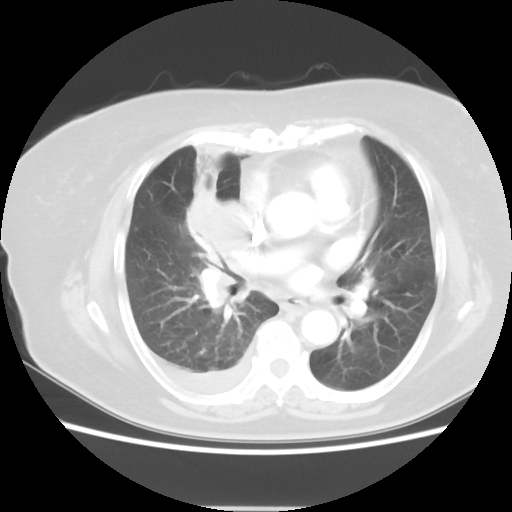
Chest CT, one axial slice. Slice 25 of 48 in the series (ordered by position). 120 kVp. Lung window (W 1500 / L -600 HU). 5 mm slice thickness. 512 × 512 image matrix, field of view 360 × 360 mm. Patient: female, 73 years. Case-level facts recorded for this patient, not image findings: clinical TNM (as recorded): T3 N3 M1b.
Outlined on this slice (bounding box drawn by a radiologist):
- lung tumour (recorded histology: small cell carcinoma): bounding box [x1, y1, x2, y2] px = [192, 186, 270, 313]